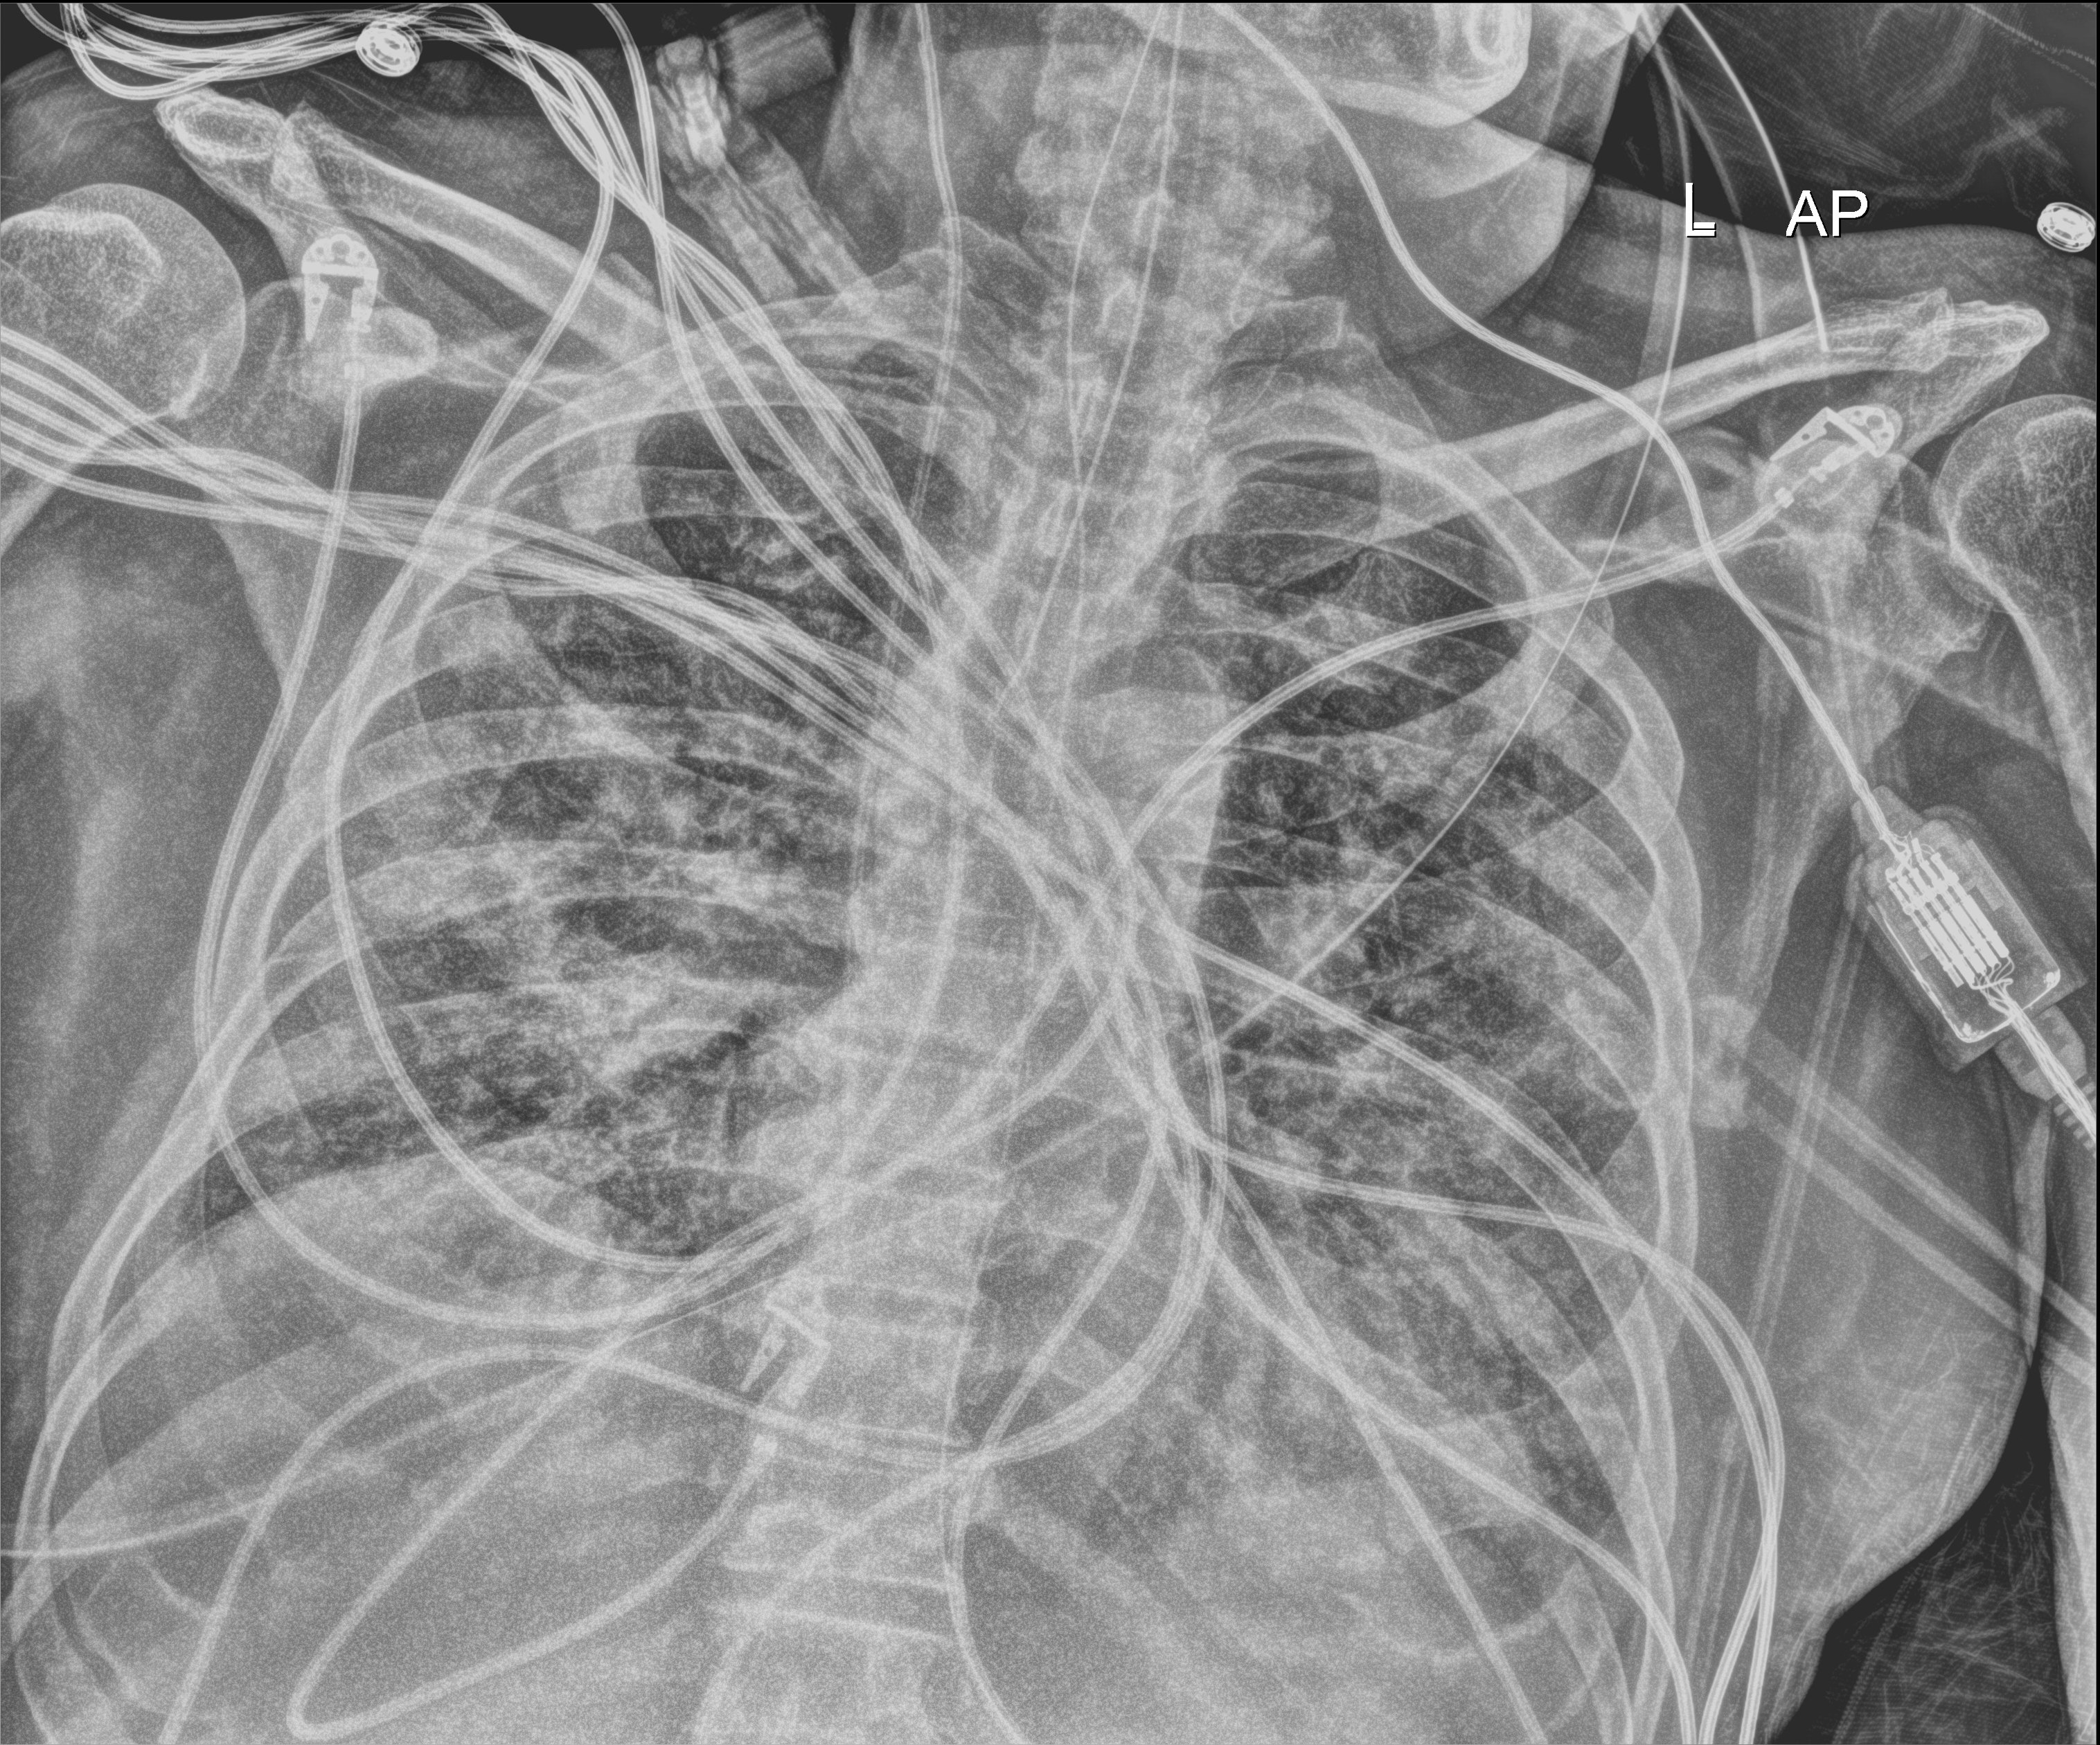
Chest X-ray (portable), anteroposterior (AP) projection. Patient hospitalised with COVID-19; male, aged 75–90 years.
From the hospital-stay record, not from the radiograph (when in the stay this image was taken is not recorded): admitted to intensive care during this hospital stay: yes.